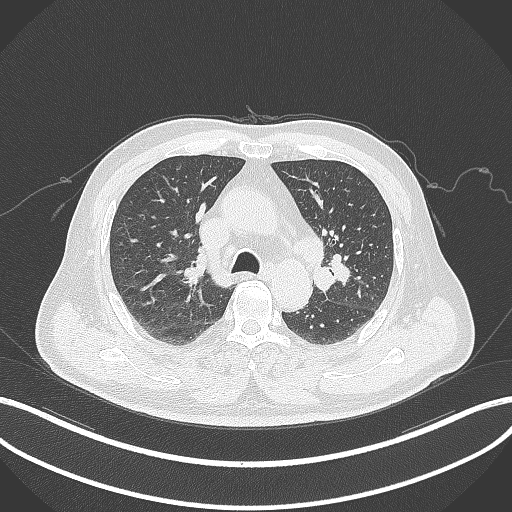
Chest CT, one axial slice. Position 201 of 286 along the scan axis. 120 kVp. Lung window (W 1500 / L -600 HU). 1 mm slice thickness. 512 × 512 image matrix. Male patient, age 67 years. From the clinical record (not read from this slice): clinical TNM (as recorded): T2a N1 M0; histopathological grade: G3.
Outlined on this slice (rectangle marked by the reading radiologist):
- lung tumour (recorded histology: adenocarcinoma): box from (x=308, y=258) to (x=353, y=295) px